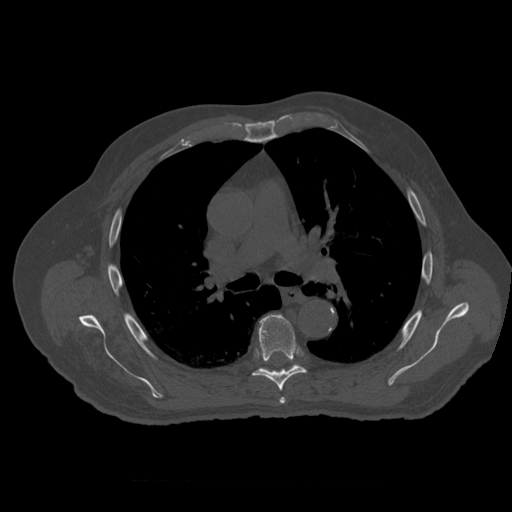
CT including the spine, one axial slice. Position 382 of 399 along the scan axis. Reconstruction kernel STANDARD. 120 kVp. Bone window (W 1800 / L 400 HU). 1.25 mm slice thickness. 512 × 512 image matrix, field of view 407 × 407 mm. Patient age 73 years. From the clinical record (not read from this slice): primary cancer: prostate; vertebrae with lytic lesions (as recorded): L2.
Structures marked on this image (semi-automatically segmented with operator editing):
- T5 vertebra: bounding box (x1, y1, x2, y2) in pixels: (280, 398, 286, 404)
- T6 vertebra: (253, 315, 306, 391)